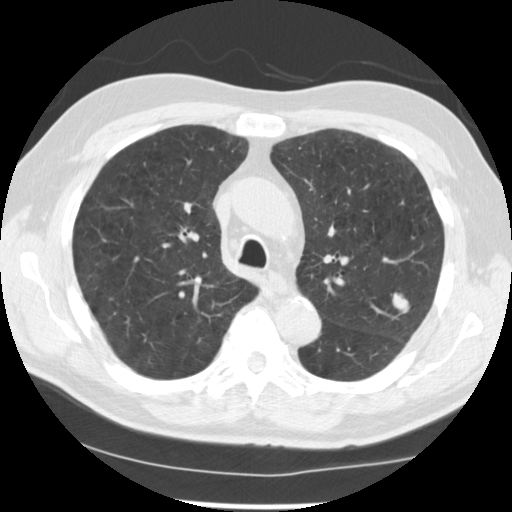
Low-dose screening chest CT, one axial slice; position 170 of 249 along the scan axis; reconstruction kernel STANDARD; lung window (W 1500 / L -600 HU); 512 × 512 image matrix.
Outlined on this slice (expert manual segmentation):
- lesion 1 (tumor, upper lobe of left lung): box from (x=392, y=293) to (x=409, y=313) px